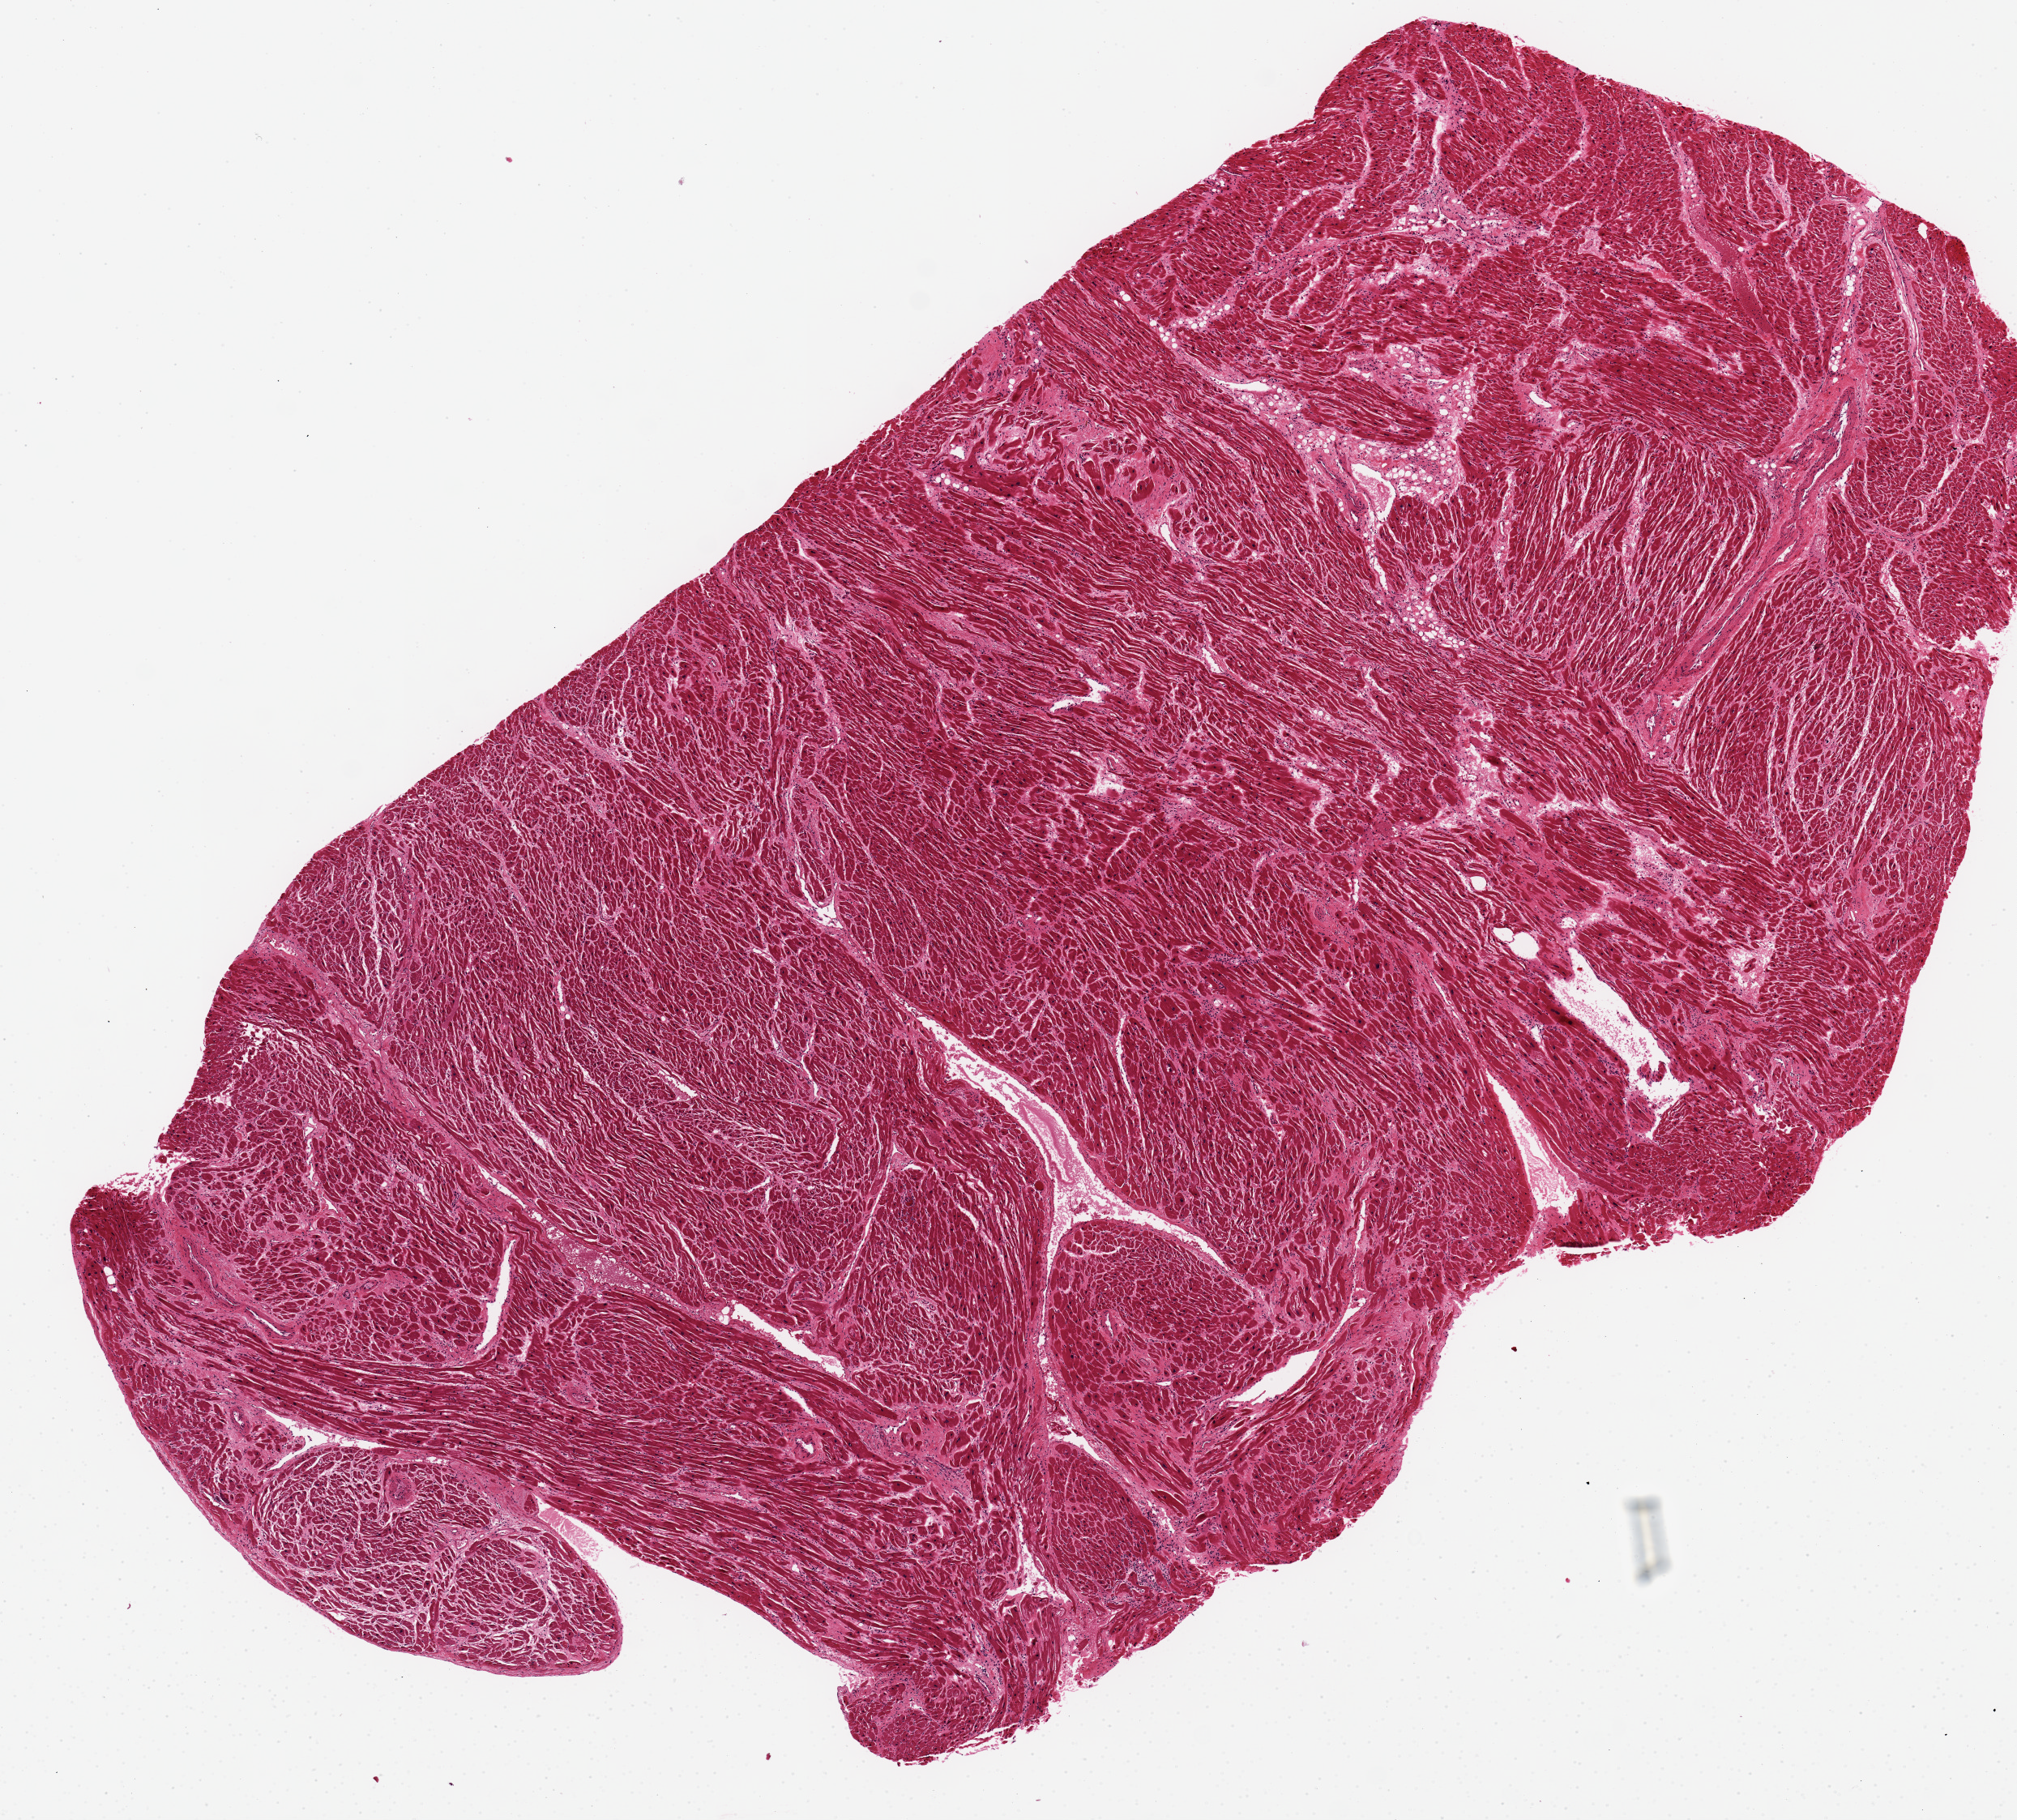
Hematoxylin and eosin (H&E) whole-slide image, low-resolution overview of the scanned area, about 9.8 x 8.9 mm, PAXgene-fixed, paraffin-embedded tissue, sampled site (target tissue): heart, tissue donor sample. Female donor.
Pathologist's review note for this sample: Minimal ischemic changes.